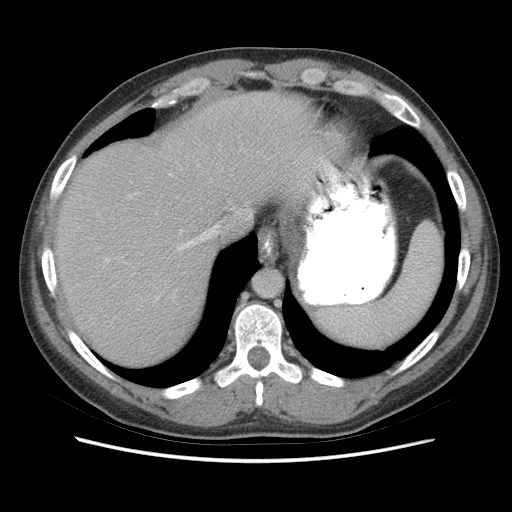
Contrast-enhanced abdominal CT (liver protocol), one axial slice. Position 59 of 73 along the scan axis. Reconstruction kernel STANDARD. Soft-tissue window (W 400 / L 40 HU). 2.5 mm slice thickness. 512 × 512 image matrix, field of view 360 × 360 mm. Case-level facts recorded for this patient, not image findings: diagnosis: hepatocellular carcinoma (patient treated with transarterial chemoembolisation; whether this scan precedes or follows treatment is not stated here); TNM stage (as recorded): Stage-IIIA; Child-Pugh class: A; tumour size: 6.6 cm.
Structures marked on this image (semi-automatically segmented with operator editing):
- abdominal aorta: box from (x=254, y=269) to (x=283, y=296) px
- liver parenchyma outside the tumour (the mass and vessels are separate outlines, so this box may not span the whole liver): (x=54, y=92)–(x=342, y=364)
- liver vessels: (x=107, y=225)–(x=219, y=262)